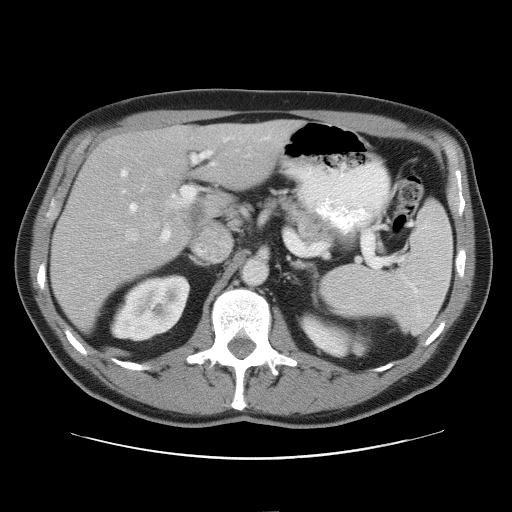
Contrast-enhanced abdominal CT, one axial slice; position 35 of 52 along the scan axis; reconstruction kernel STANDARD; intravenous contrast given; soft-tissue window (W 400 / L 40 HU); 5 mm slice thickness; 512 × 512 image matrix, field of view 393 × 393 mm. Male patient, age 70 years. From the clinical record (not read from this slice): diagnosis: colorectal cancer liver metastases, imaged before liver resection; multiple liver metastases: yes; largest metastasis: 4 cm; disease in both lobes: yes.
Annotated regions visible in this slice (expert manual segmentation):
- hepatic veins: box from (x=126, y=170) to (x=161, y=241) px
- liver: (x=52, y=121)–(x=300, y=332)
- planned liver remnant (the part of the liver to remain after resection): (x=107, y=121)–(x=300, y=191)
- portal vein (with intrahepatic branches): (x=120, y=136)–(x=273, y=243)
- liver metastasis: (x=184, y=204)–(x=208, y=228)